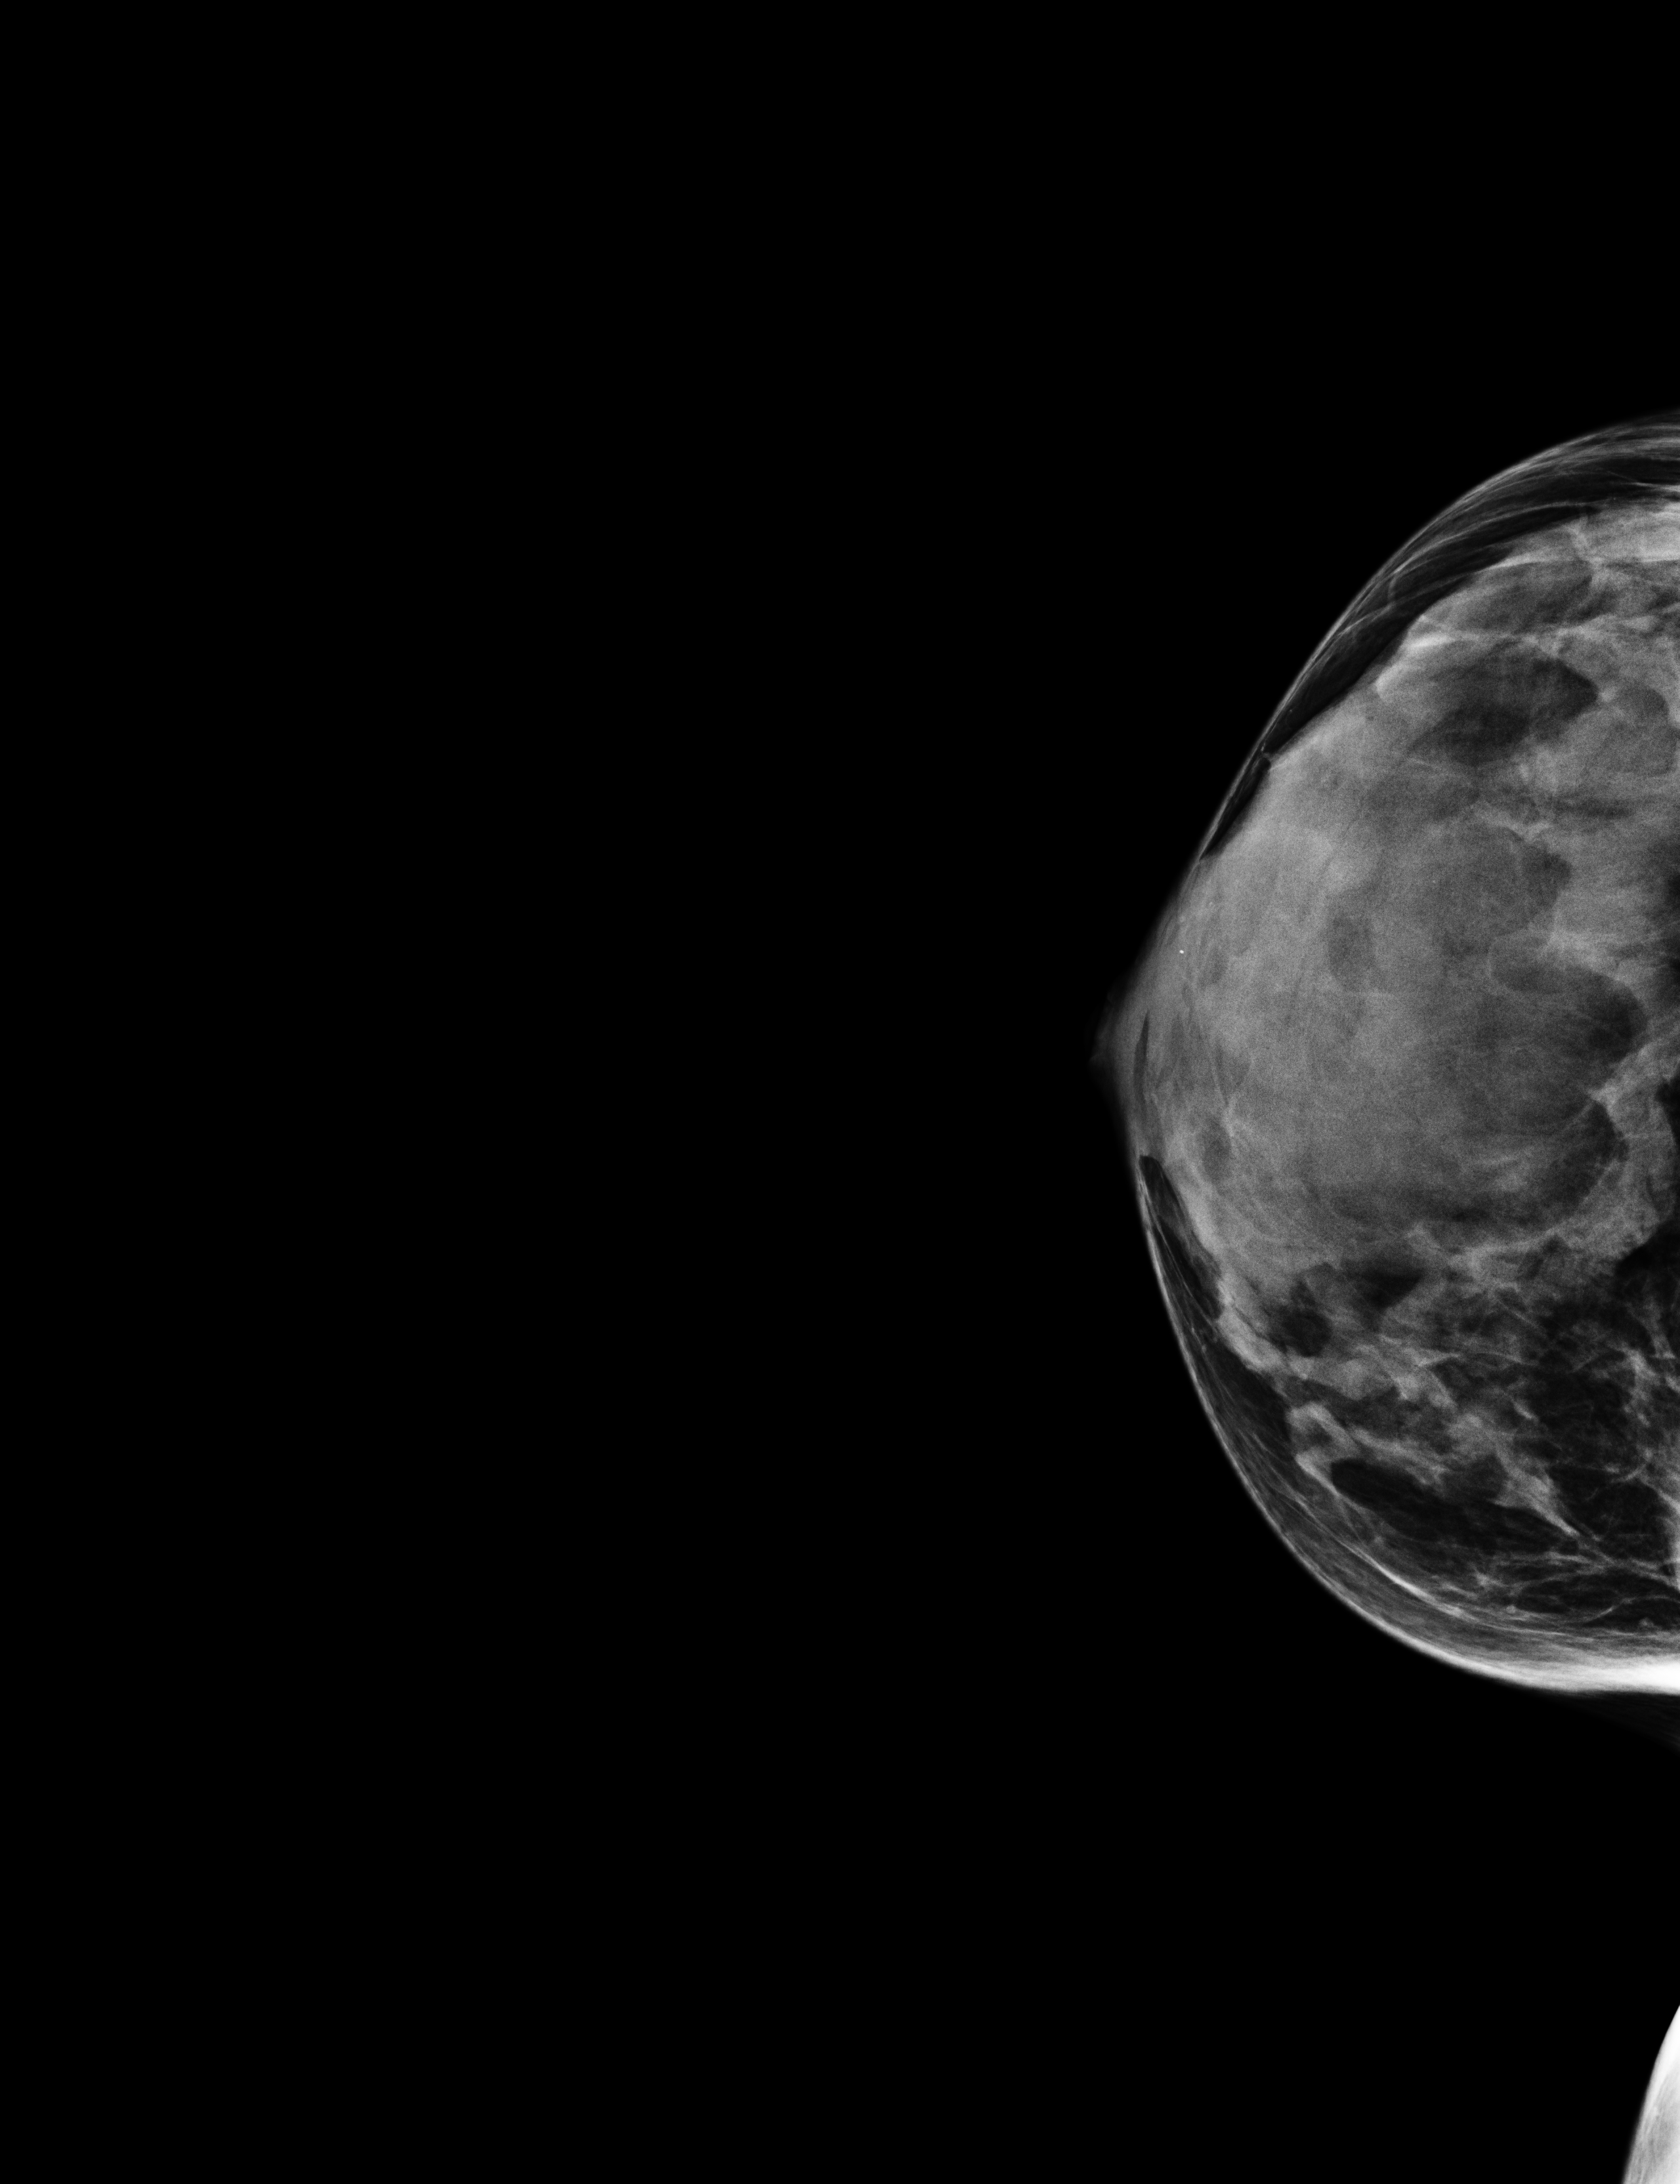
Annual screening mammography examination; compressed breast thickness 46 mm. Female patient, age 59 years.
Image type: full-field digital mammogram. Breast: right. Projection: craniocaudal (CC) view.